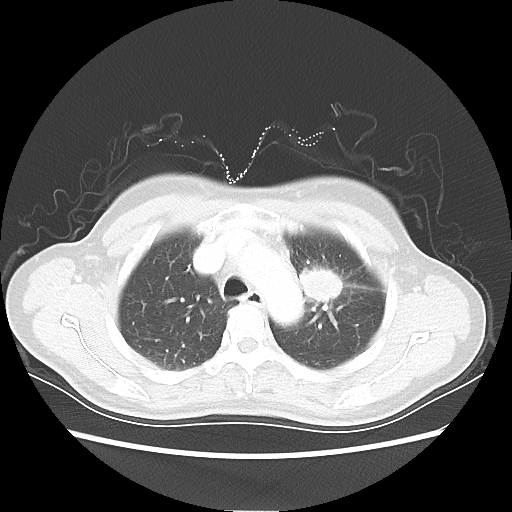
Chest CT, one axial slice. Slice 41 of 54 in the series (ordered by position). 80 kVp. Lung window (W 1500 / L -600 HU). 512 × 512 image matrix, field of view 360 × 360 mm. Female patient, age 53 years. Case-level facts recorded for this patient, not image findings: clinical TNM (as recorded): T1c N0 M0.
Outlined on this slice (bounding box drawn by a radiologist):
- lung tumour (recorded histology: adenocarcinoma): bounding box <294,262,356,312> (left, top, right, bottom; pixels)
- lung tumour (recorded histology: adenocarcinoma): <298,259,347,306>